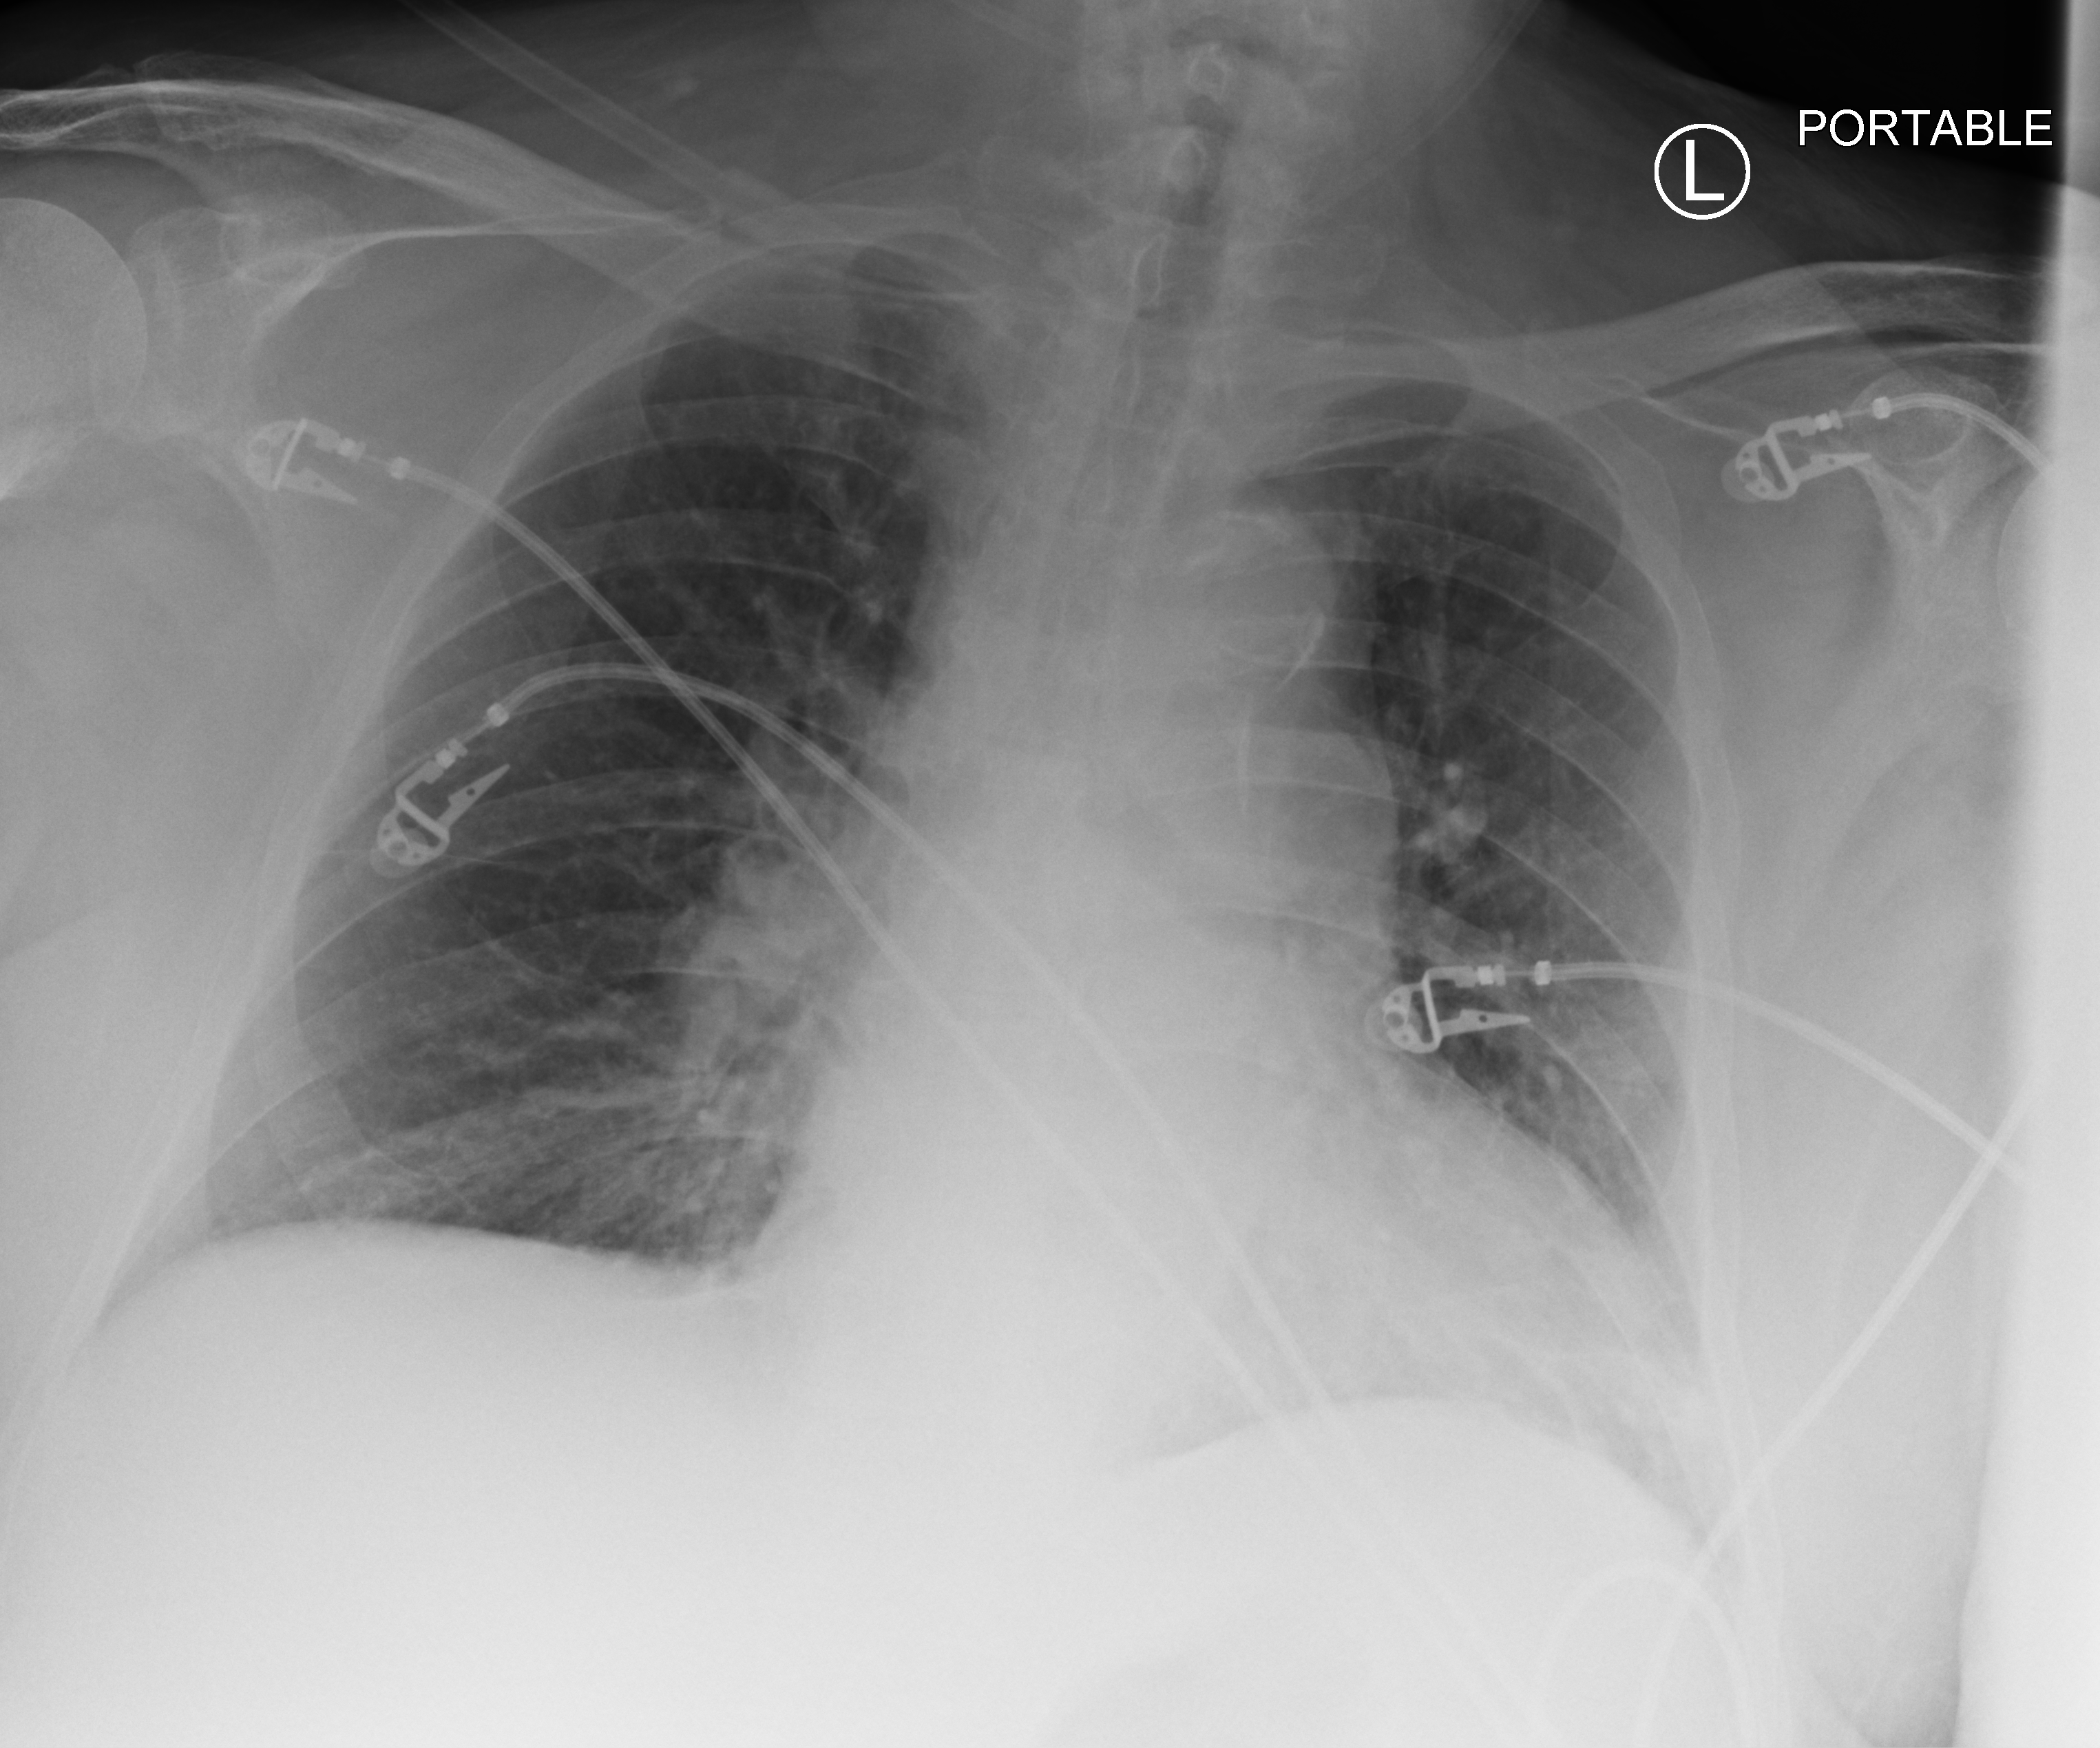
Portable chest radiograph; anteroposterior (AP) projection. Patient hospitalised with COVID-19; male, aged 75–90 years.
Hospital-stay facts (about this admission, not read from this image; timing relative to this image not recorded): admitted to intensive care during this hospital stay: no; mechanically ventilated during this hospital stay: no.